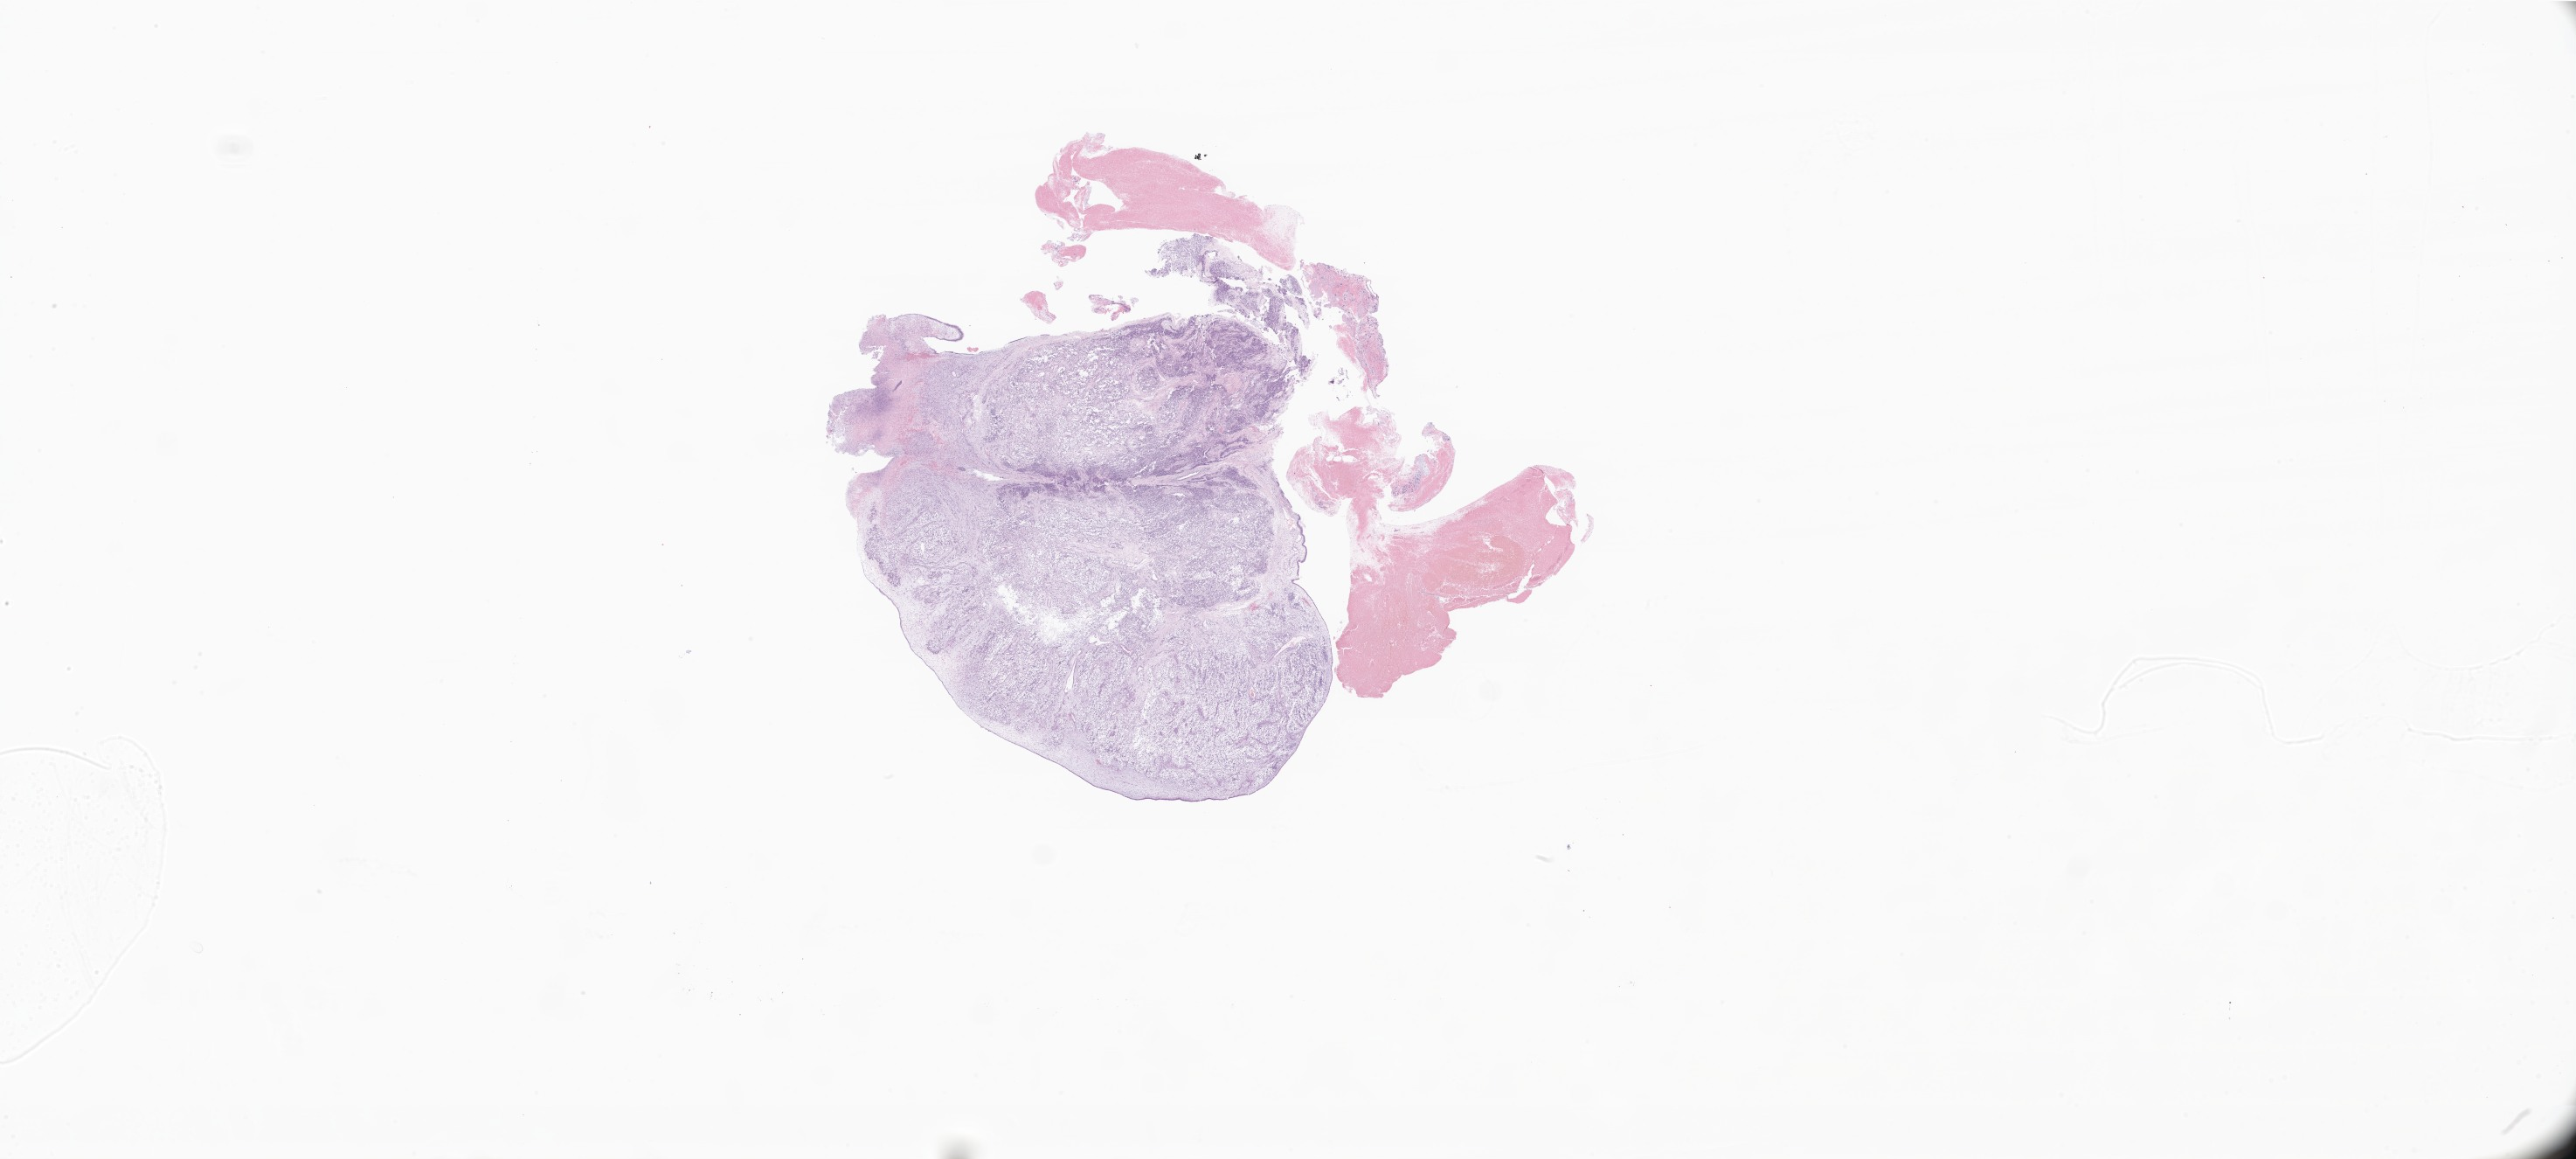
Haematoxylin and eosin whole-slide image of tumor tissue from the nasopharynx, low-resolution overview of the scanned area, about 49.7 x 22.4 mm, FFPE section. Patient female; age 73 months (6 years 1 month).
Diagnosis (ICD-O-3 morphology term): Neoplasm, malignant.